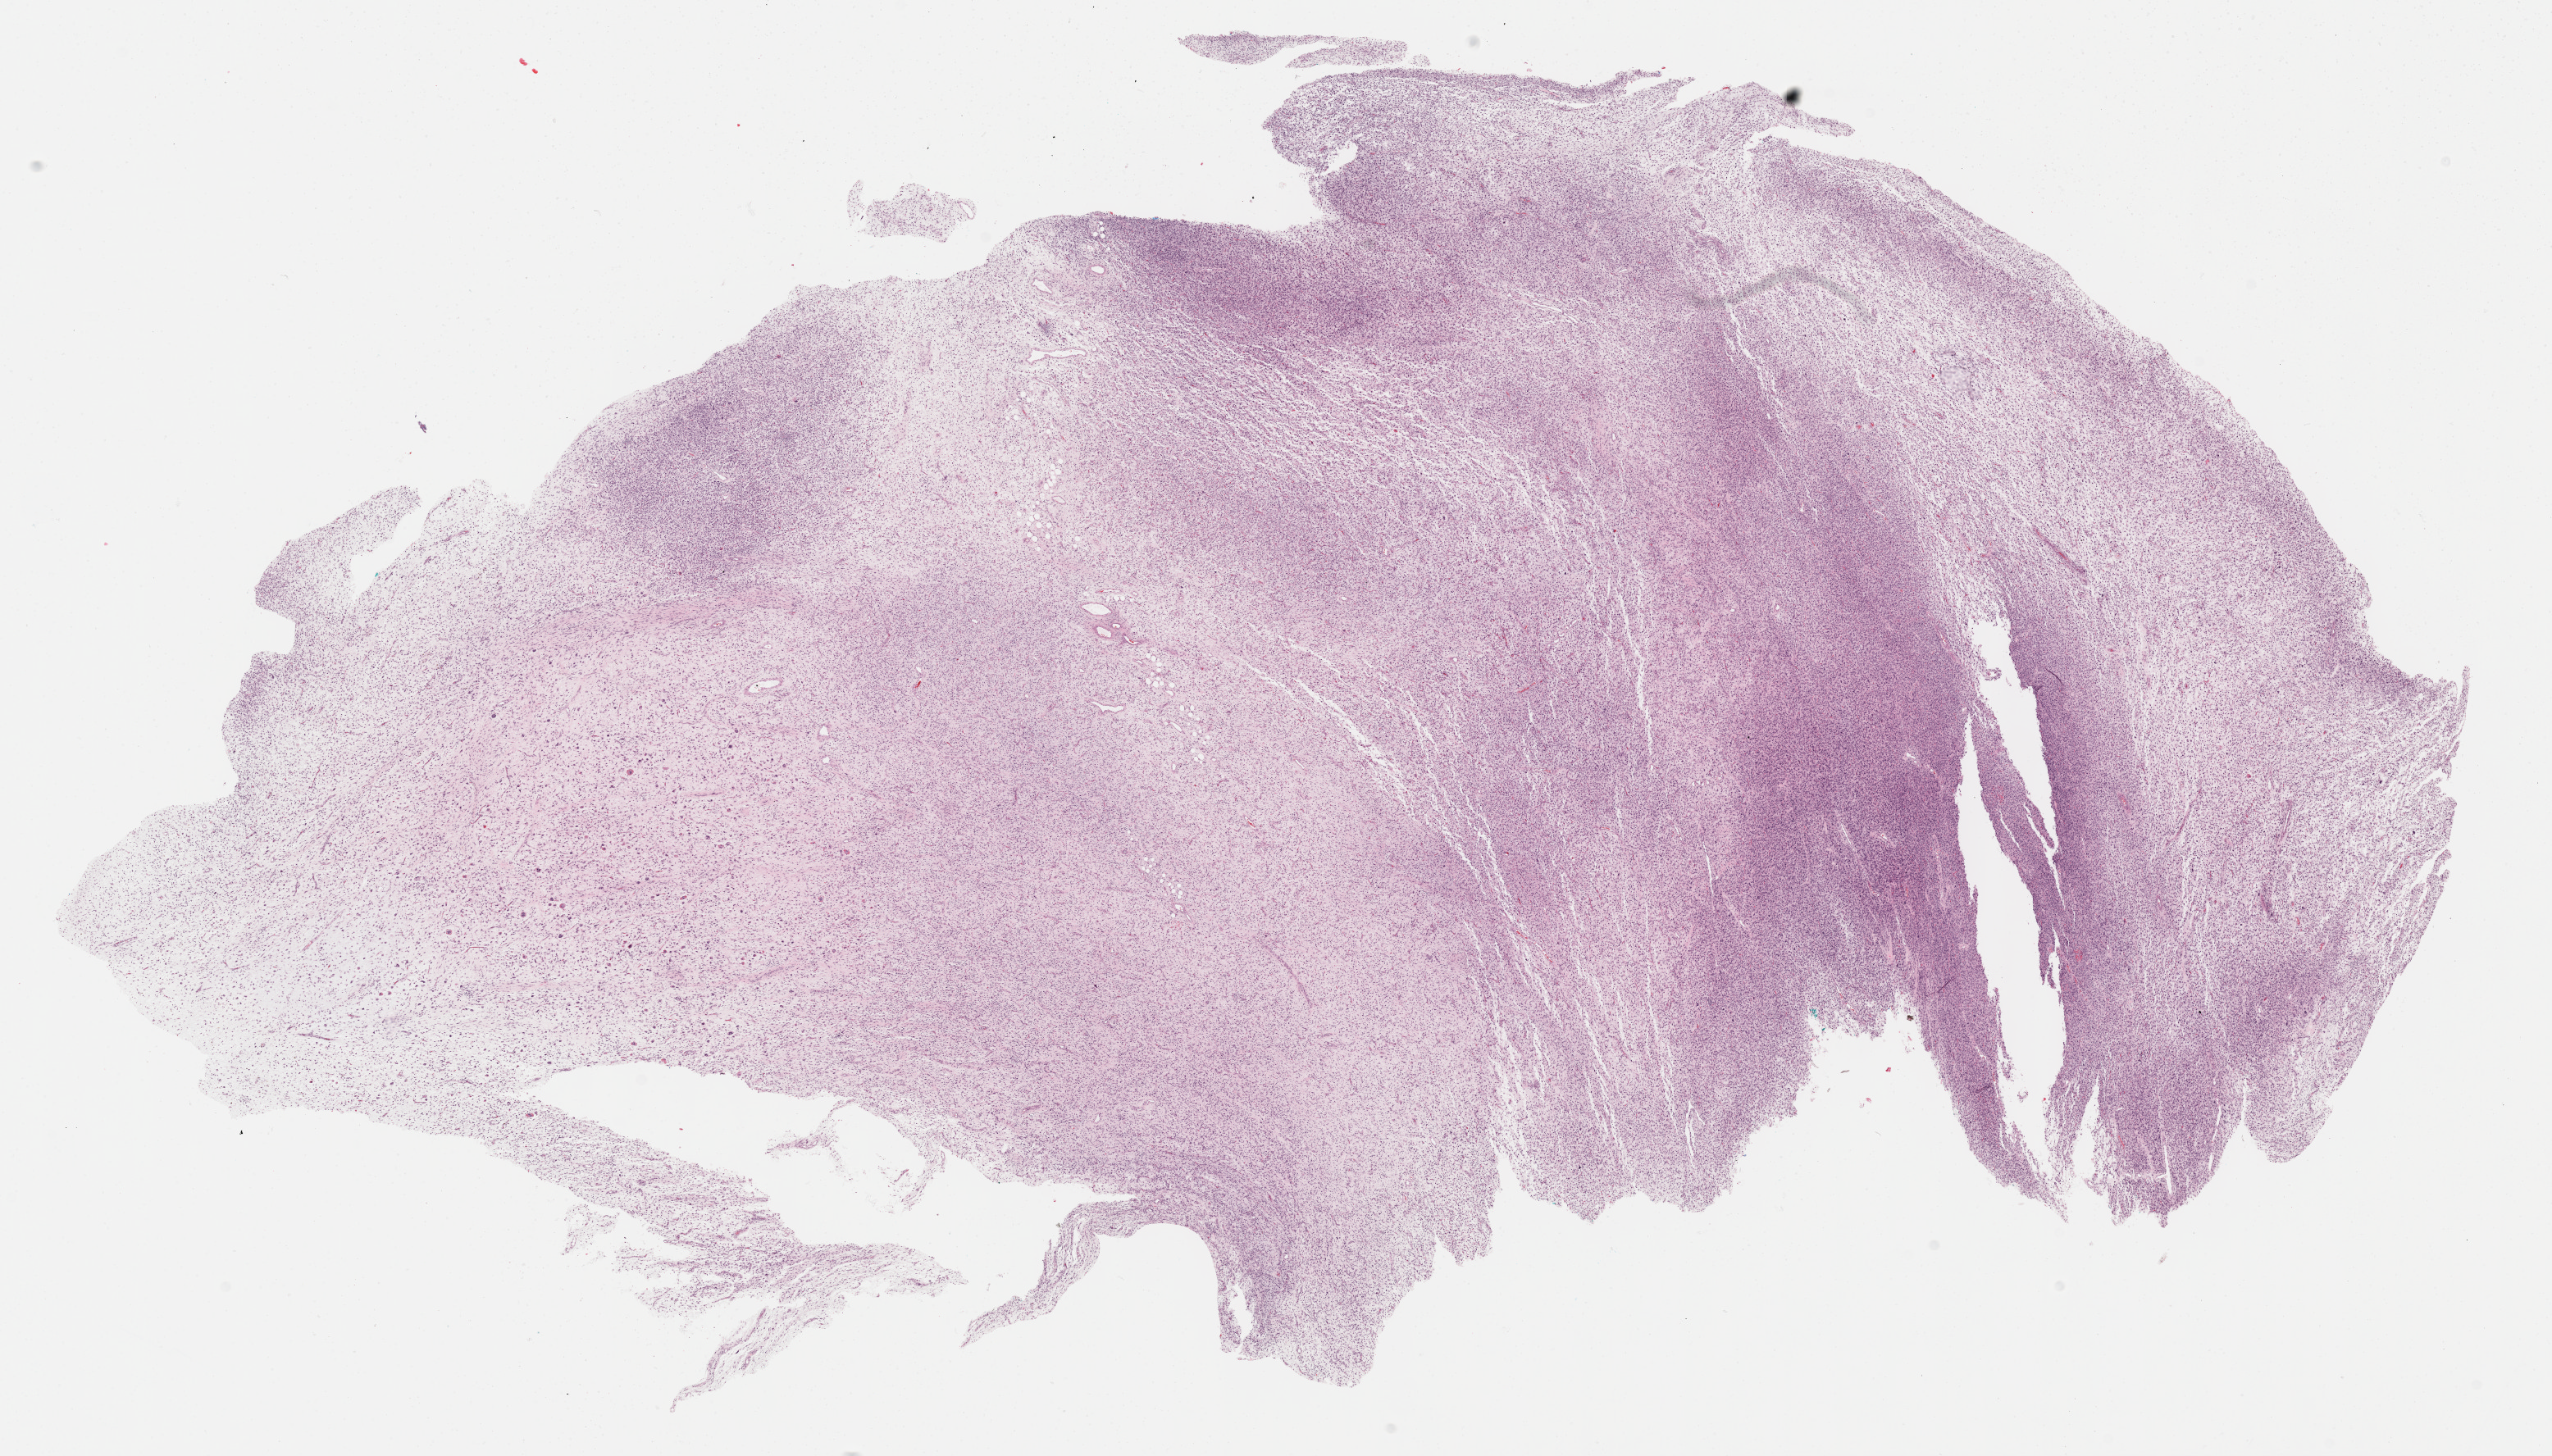
Whole-slide histology image, H&E — a low-resolution overview of the entire scanned area, about 25.2 x 14.4 mm (from a 40x scan), formalin-fixed paraffin-embedded (FFPE) diagnostic section, connective, subcutaneous and other soft tissues, primary tumour sample. Patient: female, age at initial diagnosis 54 years.
Diagnosis: Fibromyxosarcoma (connective, subcutaneous and other soft tissues of lower limb and hip).